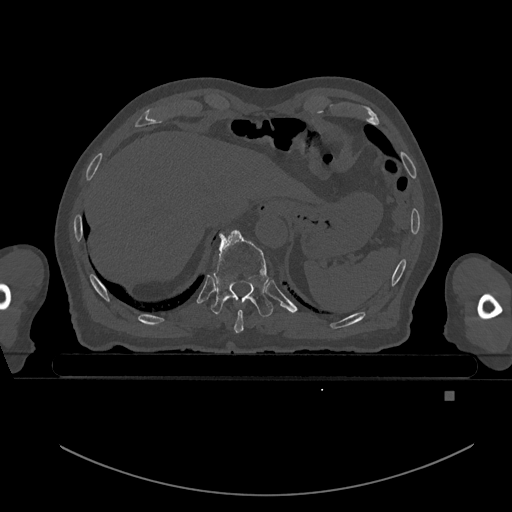
CT including the spine, one axial slice; slice 104 of 969 in the series (ordered by position); bone window (W 1800 / L 400 HU); 0.5 mm slice thickness; 512 × 512 image matrix, field of view 456 × 456 mm. Patient: male, 82 years. Case-level facts recorded for this patient, not image findings: primary cancer: prostate; vertebrae with lytic lesions (as recorded): T11, T9, T8, T2.
Annotated regions visible in this slice (semi-automatic segmentation, software-assisted and operator-edited):
- T10 vertebra: bounding box (x1, y1, x2, y2) in pixels: (211, 230, 273, 317)
- T9 vertebra: (234, 310, 243, 333)